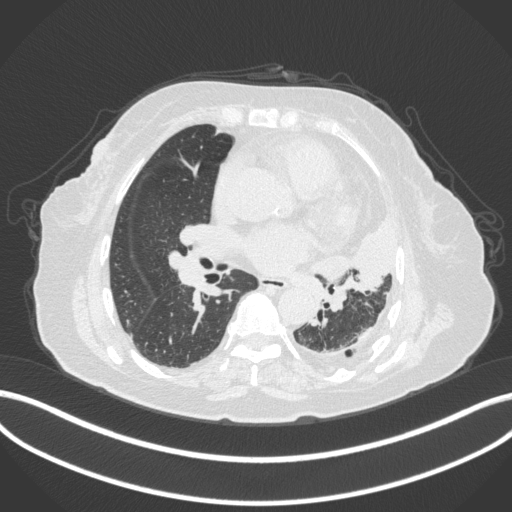
Chest CT, one axial slice; position 184 of 399 along the scan axis; 120 kVp; lung window (W 1500 / L -600 HU); 1 mm slice thickness; 512 × 512 image matrix, field of view 400 × 400 mm. Patient: female, 75 years. Case-level facts recorded for this patient, not image findings: clinical TNM (as recorded): T3 N3 M1.
Structures marked on this image (rectangle marked by the reading radiologist):
- lung tumour (recorded histology: adenocarcinoma): bounding box <308,215,396,313> (left, top, right, bottom; pixels)